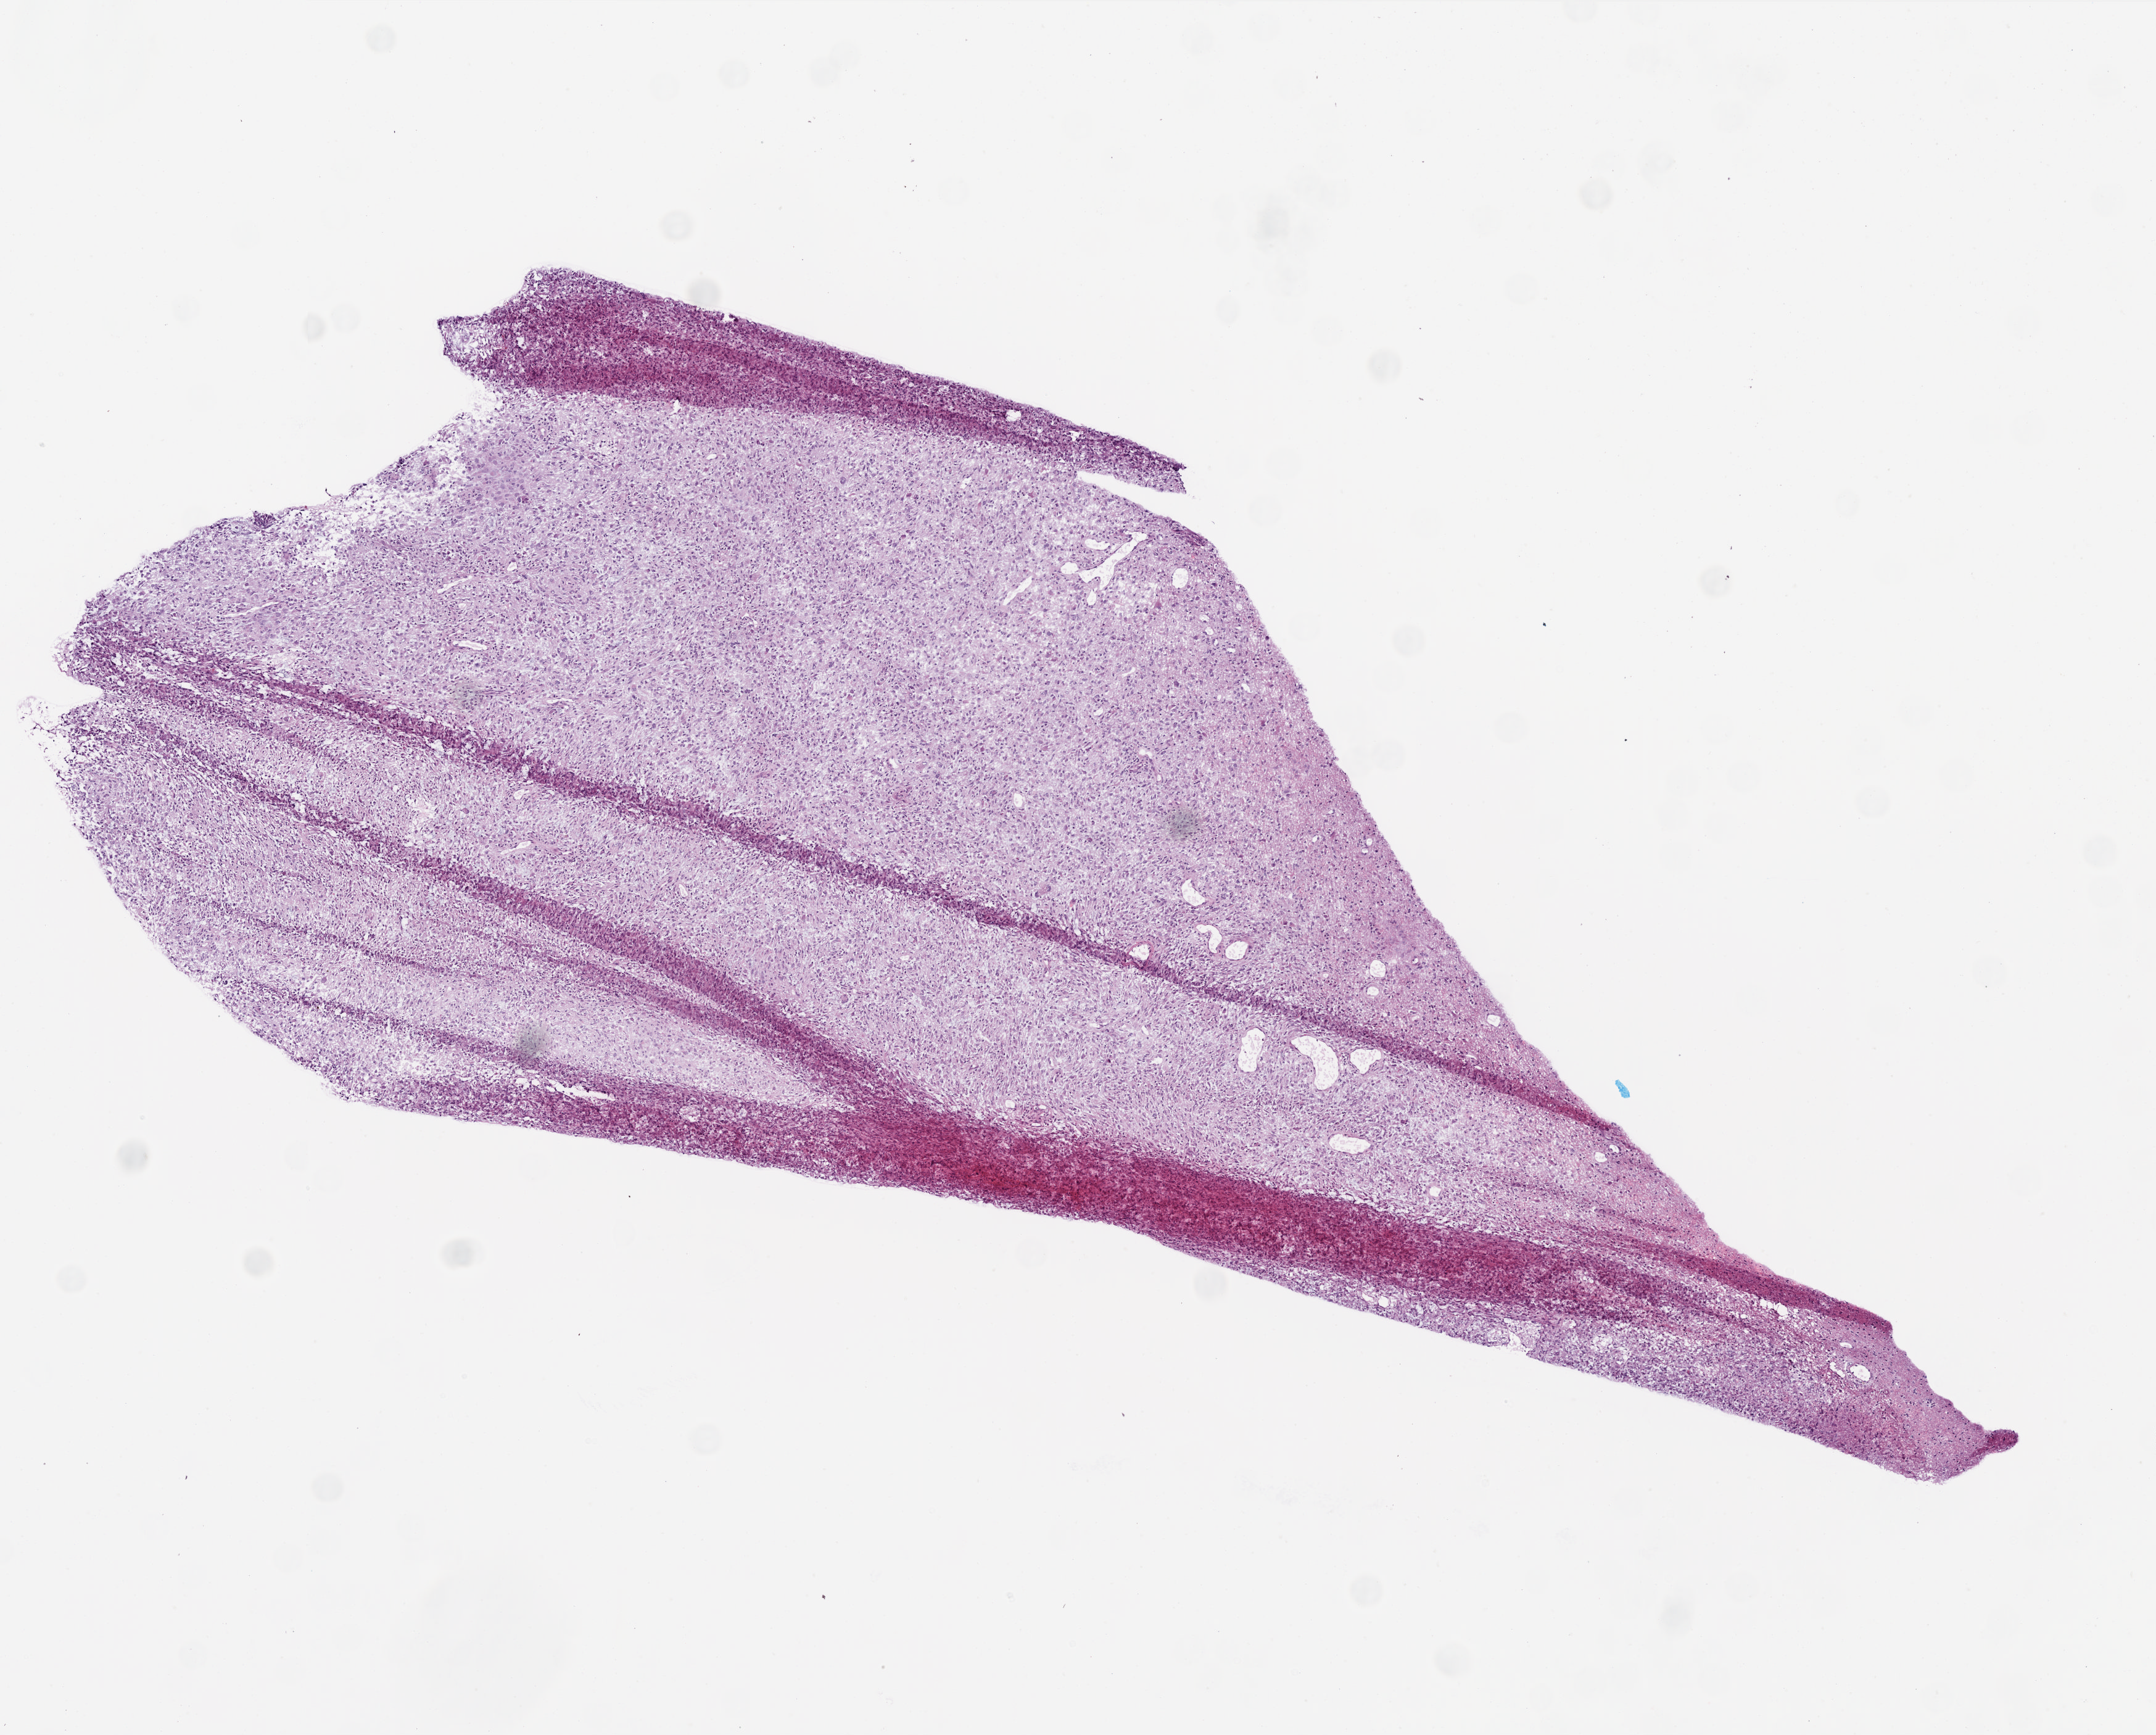
Digitized Hematoxylin and eosin (H&E) stained tissue section (whole slide), whole scanned area (about 7.0 x 5.6 mm, from a 20x scan) shown as a low-resolution overview. Frozen section from the top of the tissue portion. Brain, primary tumour sample. Patient: male, age at initial diagnosis 69 years. Pathologist review of this section (percent, as recorded): tumour cells 95%, tumour nuclei 95%, normal cells 0%, stromal cells 5%, necrosis 0%.
* histologic diagnosis: Glioblastoma